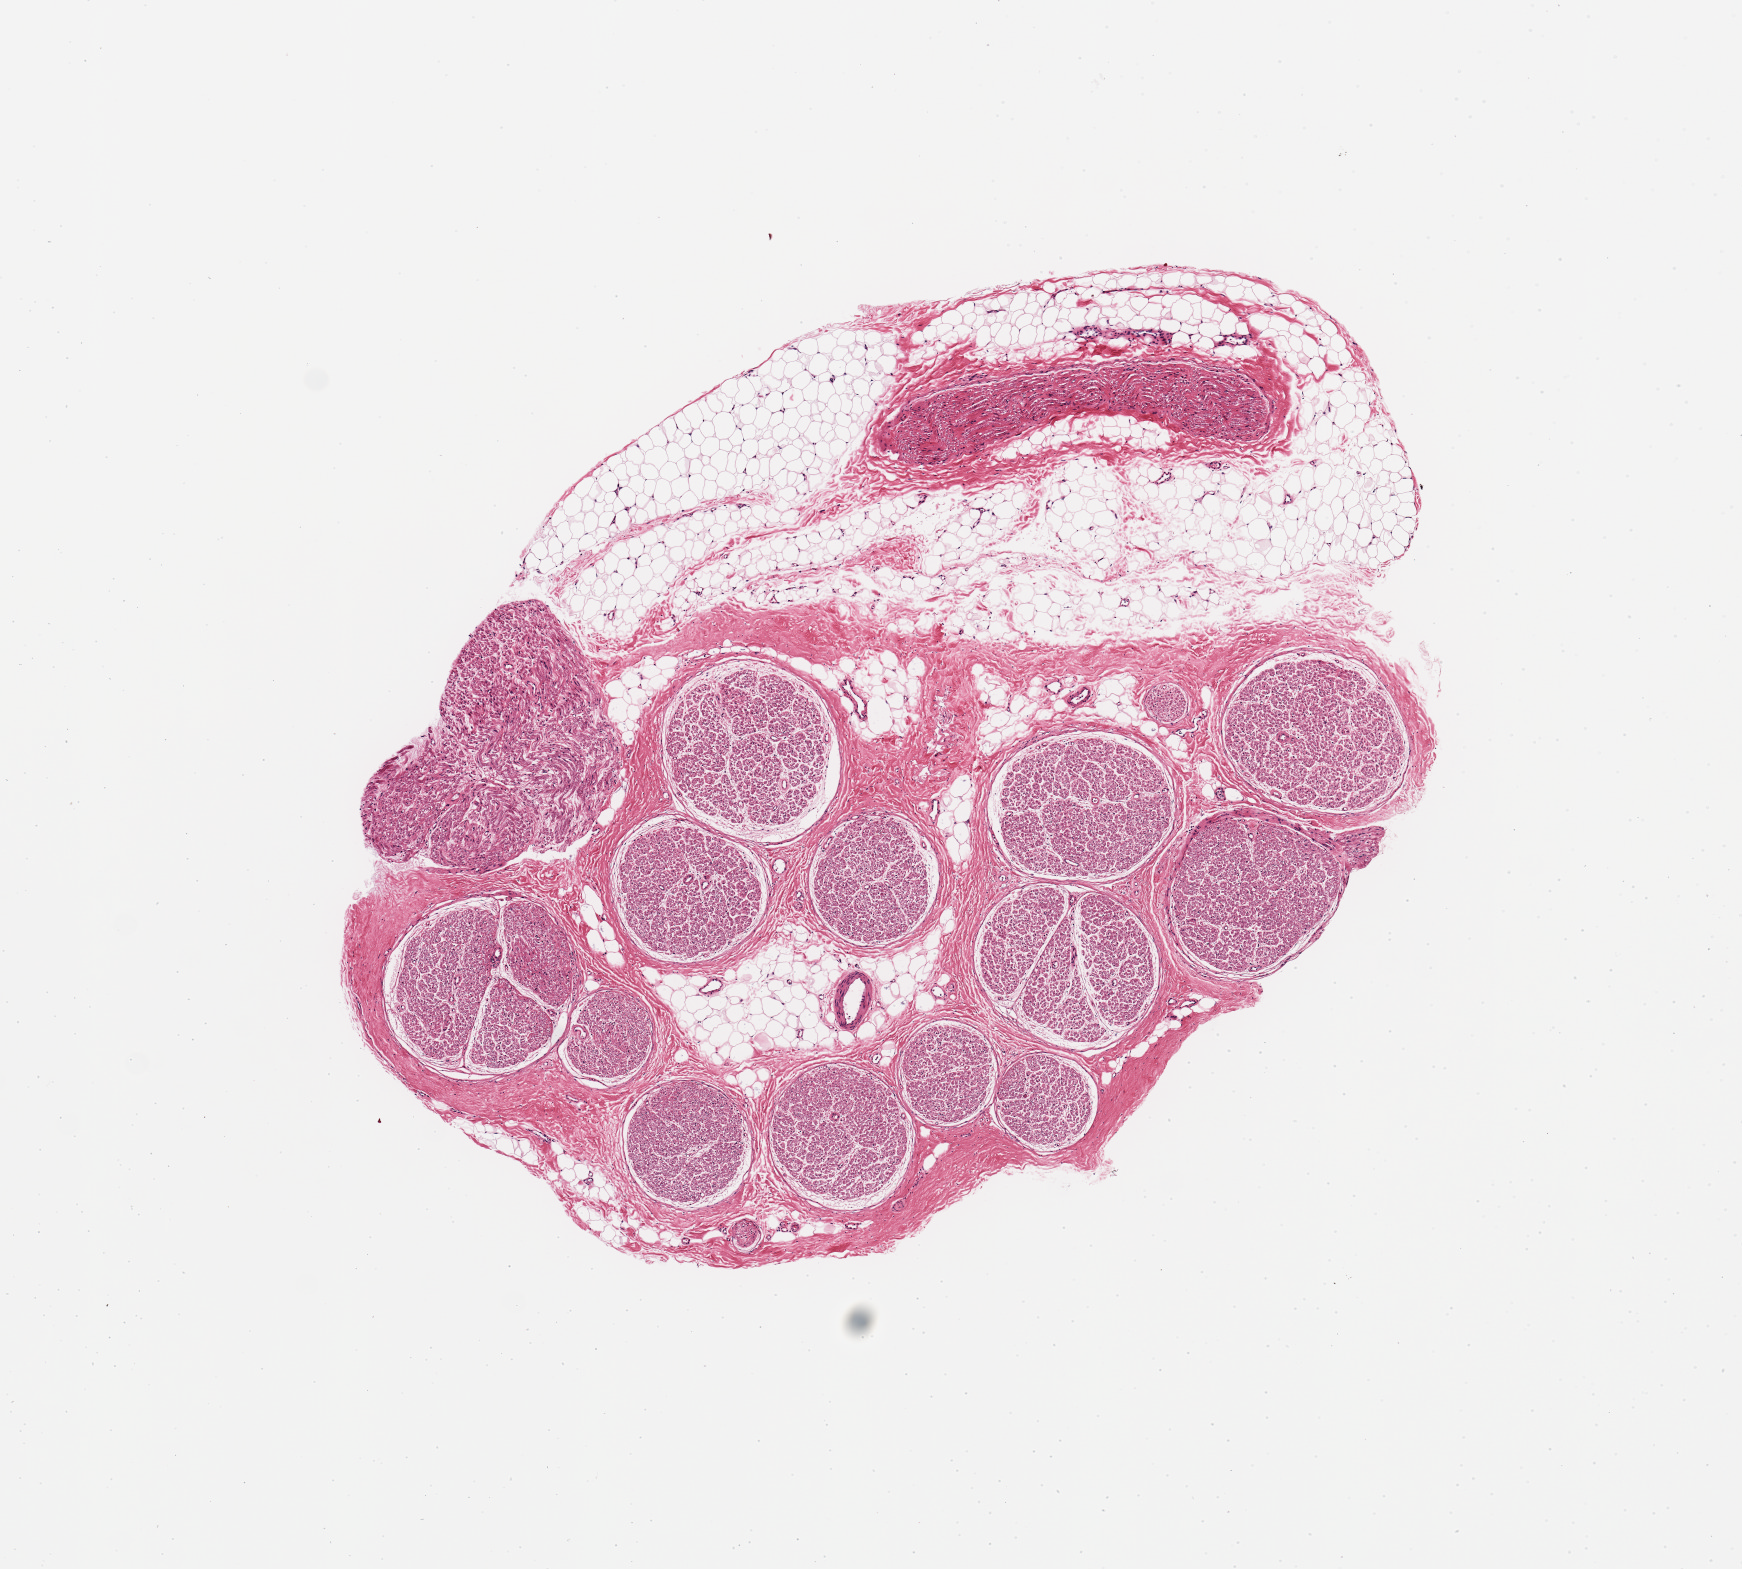
Digitized hematoxylin and eosin (H&E)-stained section, brightfield — low-resolution overview of the scanned area, about 6.9 x 6.2 mm (slide scanned at 20x), PAXgene-fixed paraffin-embedded (PFPE) section, target tissue: tibial nerve, donor tissue sample.
Pathologist's review note for this sample: 4.3x4.1mm. Specimen is 40% associated adipose tissue.